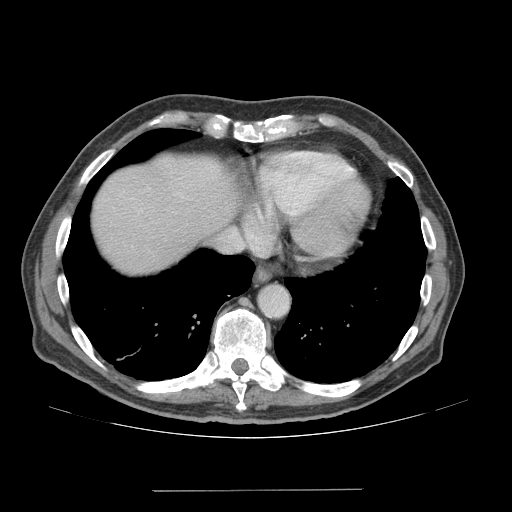
Contrast-enhanced abdominal CT (liver protocol), one axial slice; slice 64 of 77 in the series (ordered by position); soft-tissue window (W 400 / L 40 HU); 512 × 512 image matrix, field of view 400 × 400 mm. Case-level facts recorded for this patient, not image findings: diagnosis: hepatocellular carcinoma (patient treated with transarterial chemoembolisation; whether this scan precedes or follows treatment is not stated here); TNM stage (as recorded): Stage-IVA; Child-Pugh class: A; tumour nodularity: uninodular.
Outlined on this slice (semi-automatic segmentation, software-assisted and operator-edited):
- abdominal aorta: bounding box (x1, y1, x2, y2) in pixels: (260, 286, 287, 314)
- liver parenchyma outside the tumour (the mass and vessels are separate outlines, so this box may not span the whole liver): (92, 154, 236, 273)